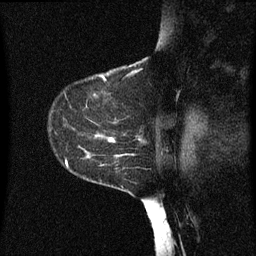
Breast MRI (dynamic contrast-enhanced), one sagittal slice. Position 46 of 60 along the scan axis. Dynamic contrast-enhanced series, image 2 of 3 at this slice position (ordered by acquisition). 1.5 T. TE 4.2 ms, TR 8 ms. 2 mm slice thickness. 256 × 256 image matrix, field of view 200 × 200 mm. Female patient, age 55 years.
Outlined on this slice (semi-automatic segmentation, software-assisted and operator-edited):
- analysis volume of interest (the breast-tissue region the enhancement analysis was run in; not a lesion): bounding box (x1, y1, x2, y2) in pixels: (48, 124, 151, 183)
- tumour enhancement mask (voxels above the 70 % enhancement threshold inside the analysis volume of interest): (86, 134, 141, 155)